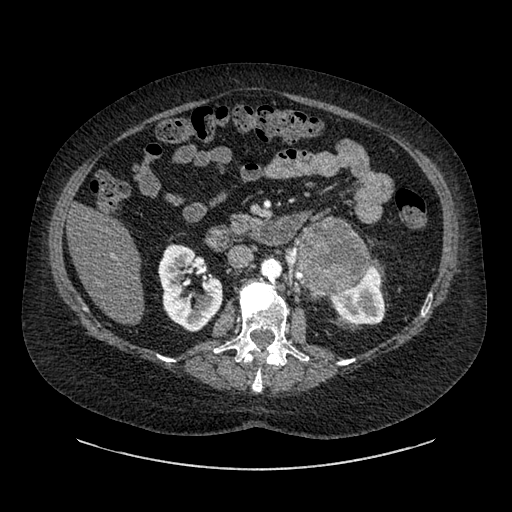
Contrast-enhanced abdominal CT, one axial slice; slice 514 of 769 in the series (ordered by position); reconstruction kernel SOFT; intravenous contrast given; soft-tissue window (W 400 / L 40 HU); 512 × 512 image matrix. Patient: female, 61 years. Case-level facts recorded for this patient, not image findings: diagnosis: adrenocortical carcinoma; tumour side: left adrenal; tumour size at pathology: 13 cm; Ki-67 index: 79 %; stage (as recorded): 2.
Outlined on this slice (semi-automatically segmented with operator editing):
- mass: bounding box (x1, y1, x2, y2) in pixels: (299, 223, 368, 294)